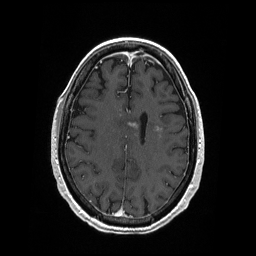
Brain MRI from a brain-tumour surgery series, one axial slice; position 75 of 208 along the scan axis; T1-weighted post-contrast; 1 mm slice thickness; 256 × 256 image matrix, field of view 256 × 256 mm. From the clinical record (not read from this slice): histopathology: Primary diffuse large B-cell lymphoma.
Structures marked on this image (manually delineated by an expert):
- tumour: bounding box (x1, y1, x2, y2) in pixels: (127, 121, 164, 132)